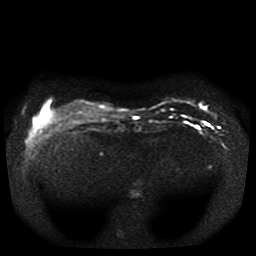
Breast MRI, one axial slice; slice 5 of 41 in the series (ordered by position); diffusion-weighted series; image 2 of 4 stored at this slice position (different b-values; order by instance number); 1.5 T; 5 mm slice thickness; 256 × 256 image matrix. Female patient.
Outlined on this slice (manually delineated by an expert):
- tumour on diffusion-weighted imaging: bounding box <199,104,207,109> (left, top, right, bottom; pixels)